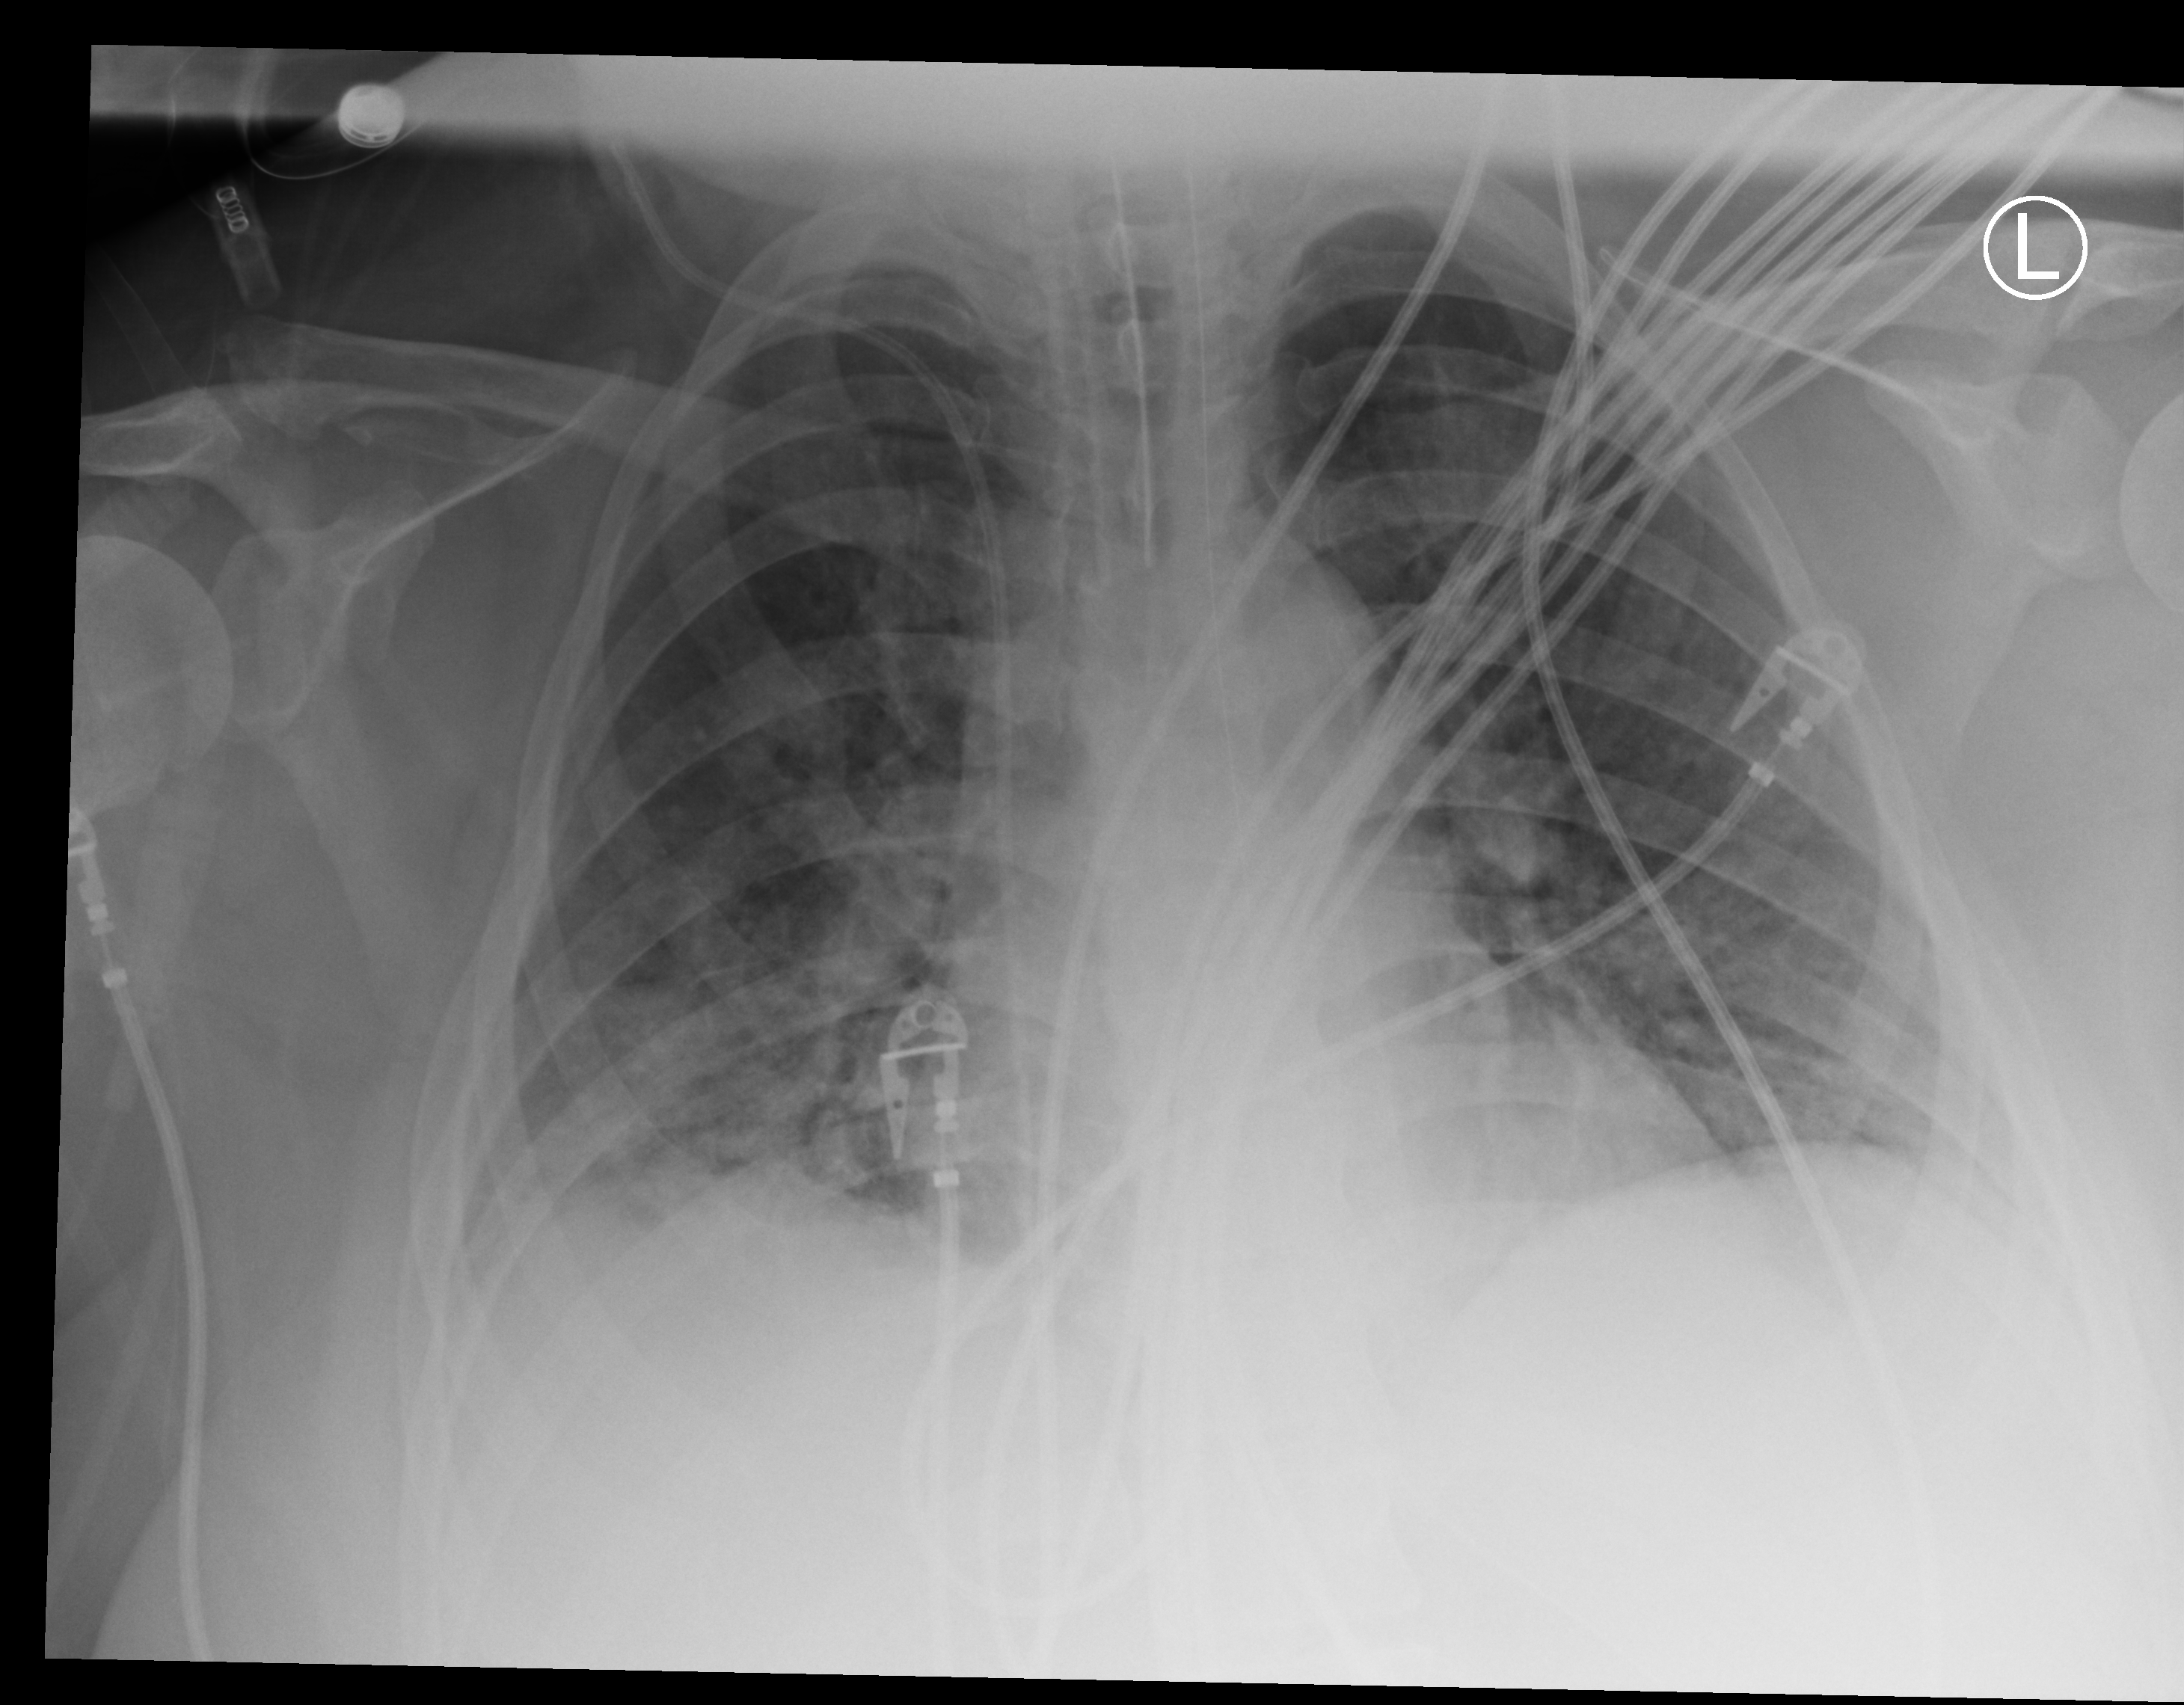
Portable chest radiograph; anteroposterior (AP) projection. Patient hospitalised with COVID-19; female, aged 18–59 years.
From the hospital-stay record, not from the radiograph (when in the stay this image was taken is not recorded): admitted to intensive care during this hospital stay: yes; diabetes (admission record): no.